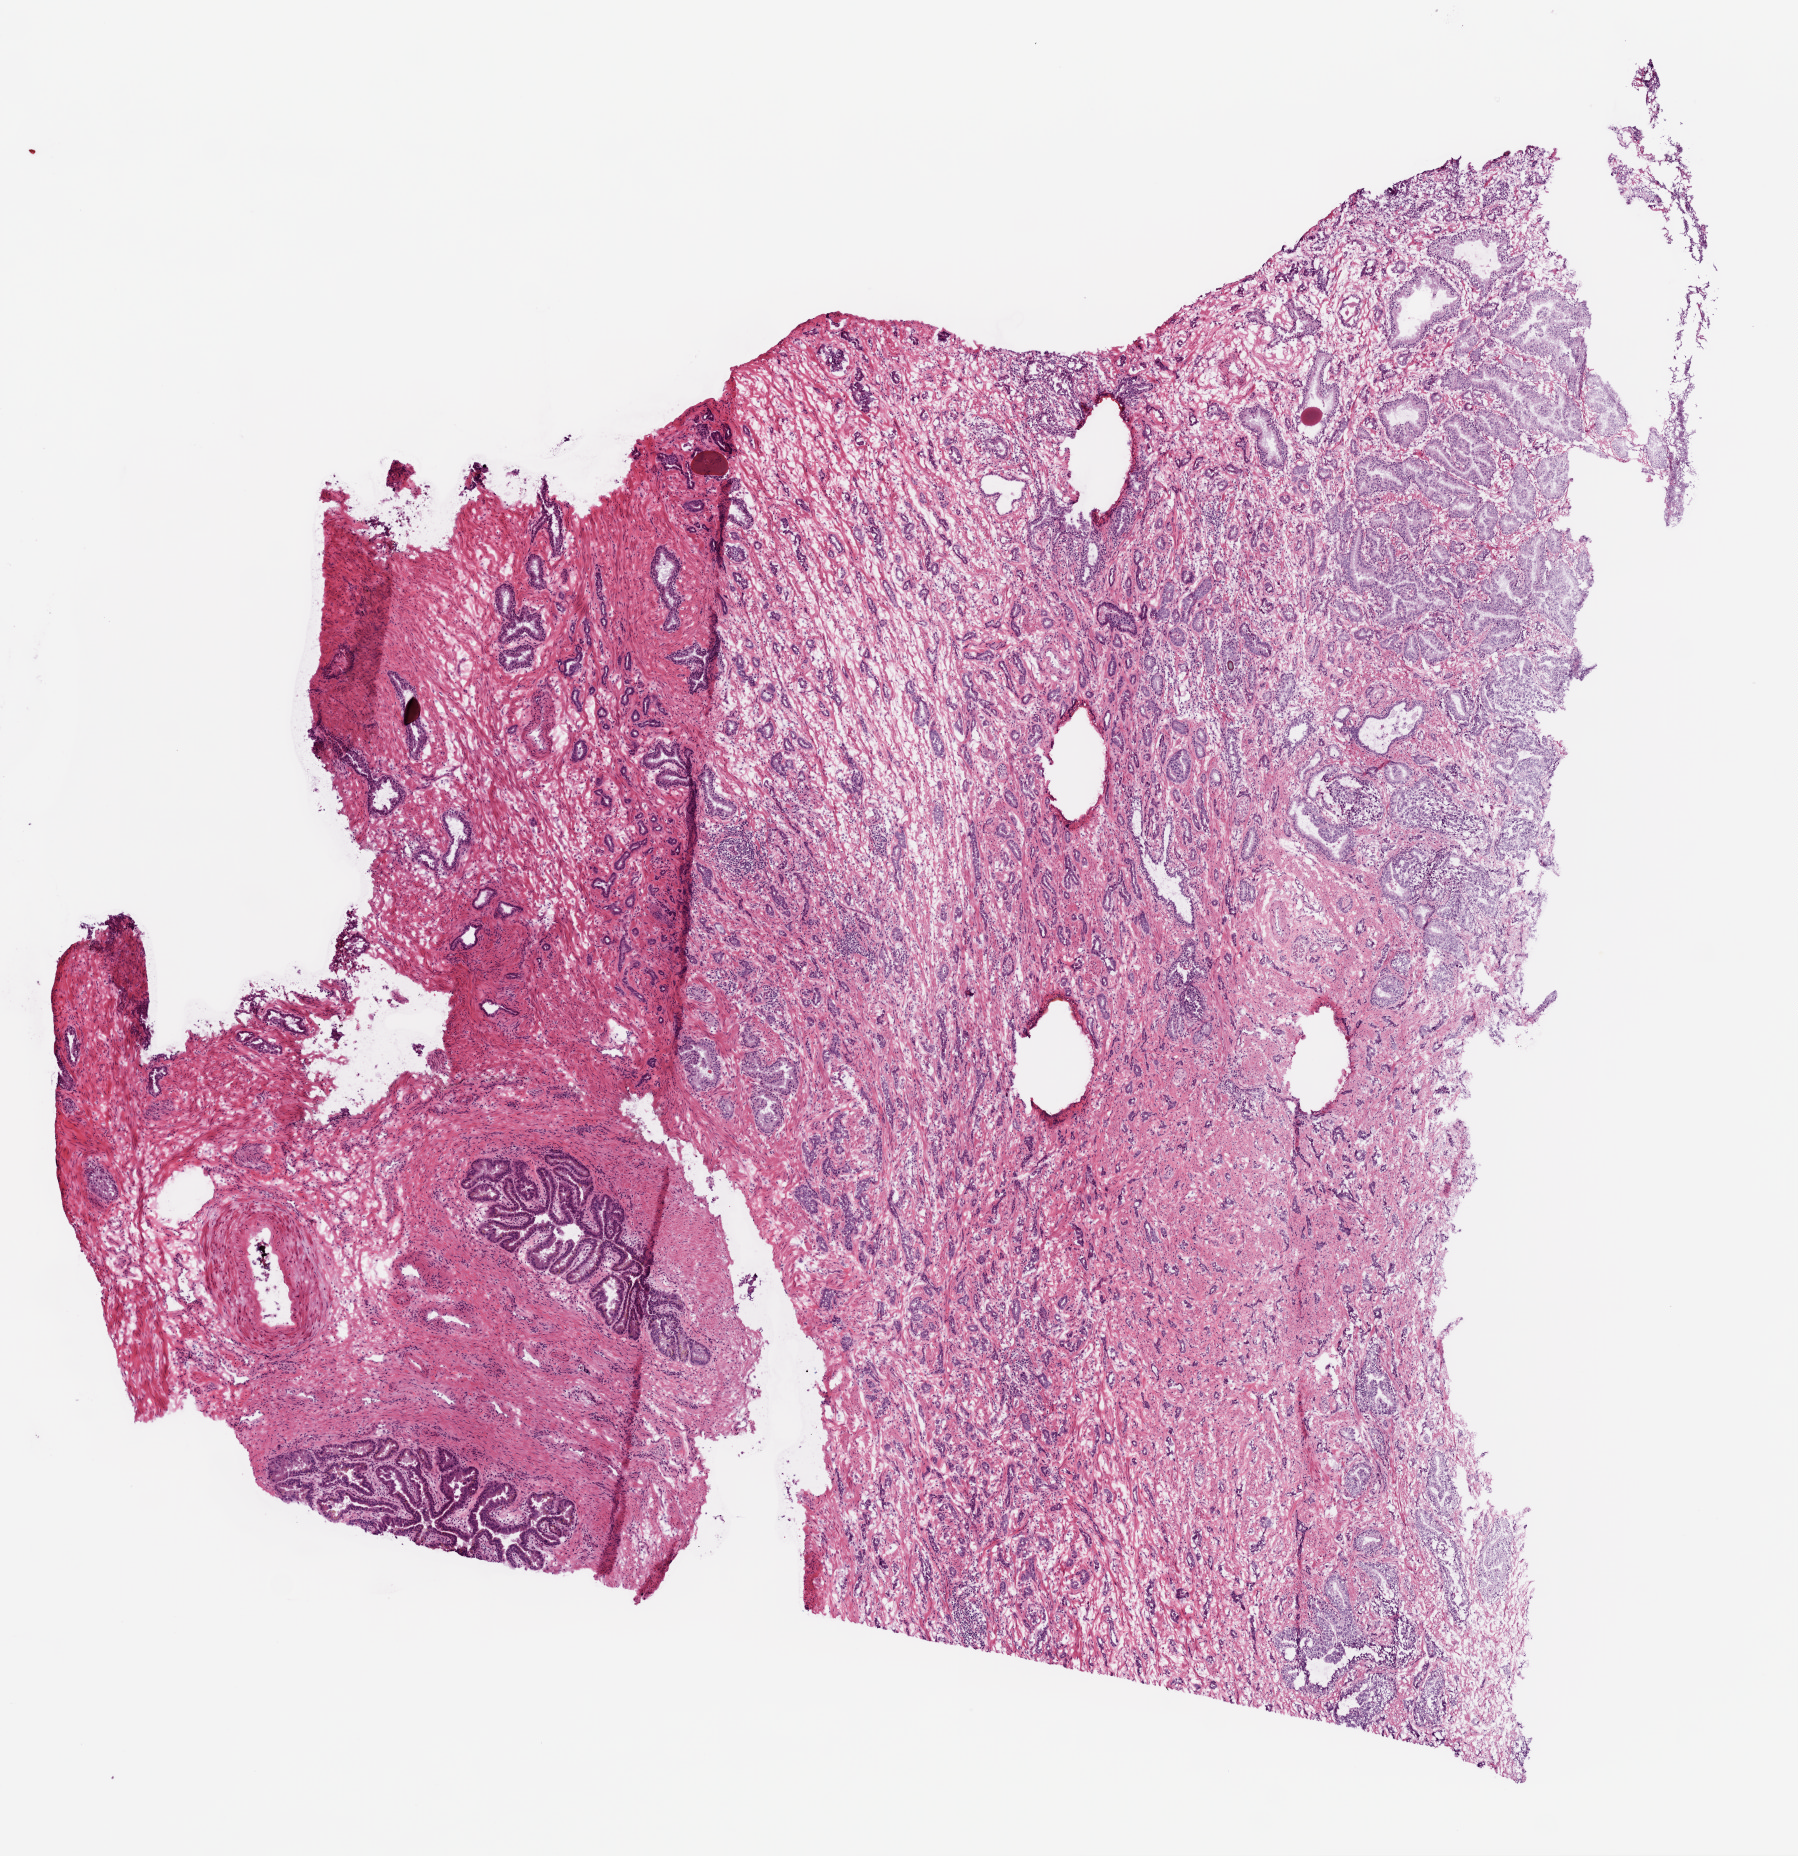
Digitized Hematoxylin and eosin (H&E) stained tissue section (whole slide), shown as a low-resolution overview of the whole scanned area (about 7.3 x 7.5 mm, from a 20x scan); frozen section; primary tumour sample from the prostate. Male patient; age at initial diagnosis 52 years. Gleason score: 7 (3+4). Pathologist review of this section (percent, as recorded): tumour cells 65%, tumour nuclei 65%, normal cells 10%, stromal cells 25%, necrosis 0%.
- lymph nodes positive (case pathology): 0 of 4 examined
- diagnosis: Acinar cell carcinoma (prostate gland)